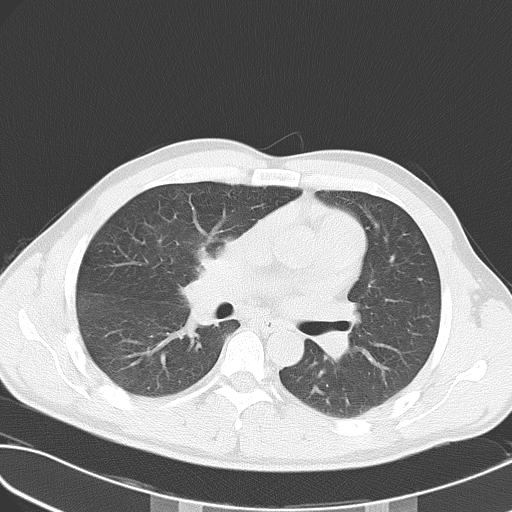
Chest CT, one axial slice. Slice 31 of 55 in the series (ordered by position). Reconstruction kernel B70f. 120 kVp. Lung window (W 1500 / L -600 HU). 512 × 512 image matrix, field of view 346 × 346 mm. Patient: male, 32 years. From the clinical record (not read from this slice): clinical TNM (as recorded): T4 N3 M0.
Structures marked on this image (bounding box drawn by a radiologist):
- lung tumour (recorded histology: small cell carcinoma): bounding box <171,222,242,333> (left, top, right, bottom; pixels)